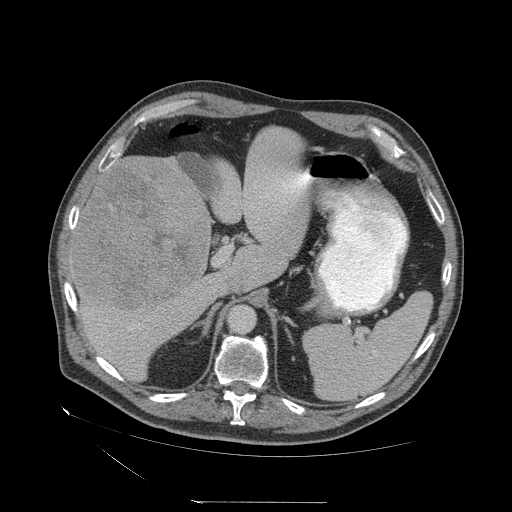
Contrast-enhanced abdominal CT (liver protocol), one axial slice. Position 36 of 83 along the scan axis. Reconstruction kernel STANDARD. Soft-tissue window (W 400 / L 40 HU). 2.5 mm slice thickness. 512 × 512 image matrix, field of view 460 × 460 mm. Case-level facts recorded for this patient, not image findings: diagnosis: hepatocellular carcinoma (patient treated with transarterial chemoembolisation; whether this scan precedes or follows treatment is not stated here); TNM stage (as recorded): Stage-I; Child-Pugh class: A; tumour differentiation: well differentiated; tumour nodularity: uninodular.
Annotated regions visible in this slice (semi-automatically segmented with operator editing):
- liver parenchyma outside the tumour (the mass and vessels are separate outlines, so this box may not span the whole liver): bounding box <68,156,306,380> (left, top, right, bottom; pixels)
- mass: <71,155,211,311>
- liver vessels: <107,163,292,329>